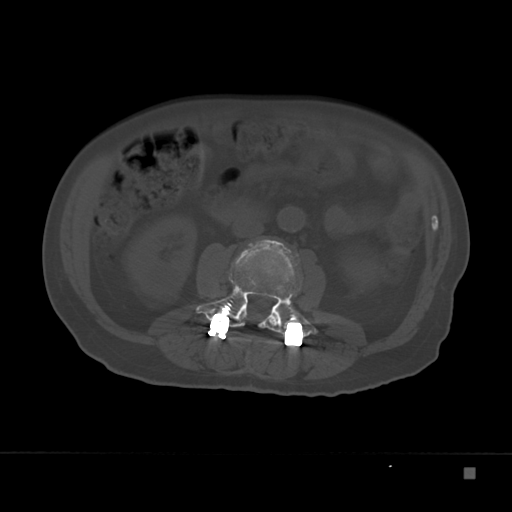
CT including the spine, one axial slice; slice 74 of 332 in the series (ordered by position); 120 kVp; bone window (W 1800 / L 400 HU); 1.5 mm slice thickness; 512 × 512 image matrix. Patient: male, 72 years. Case-level facts recorded for this patient, not image findings: primary cancer: skeletal.
Structures marked on this image (semi-automatic segmentation, software-assisted and operator-edited):
- L2 vertebra: bounding box <240,308,277,326> (left, top, right, bottom; pixels)
- L3 vertebra: <196,239,317,338>